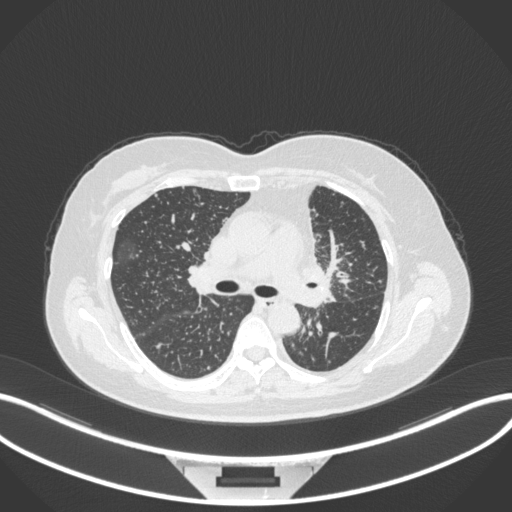
Chest CT, one axial slice; position 206 of 348 along the scan axis; reconstruction kernel B31f; lung window (W 1500 / L -600 HU); 512 × 512 image matrix. Female patient, age 49 years. From the clinical record (not read from this slice): clinical TNM (as recorded): T1c N0 M1.
Outlined on this slice (bounding box drawn by a radiologist):
- lung tumour (recorded histology: adenocarcinoma): box from (x=297, y=253) to (x=340, y=311) px